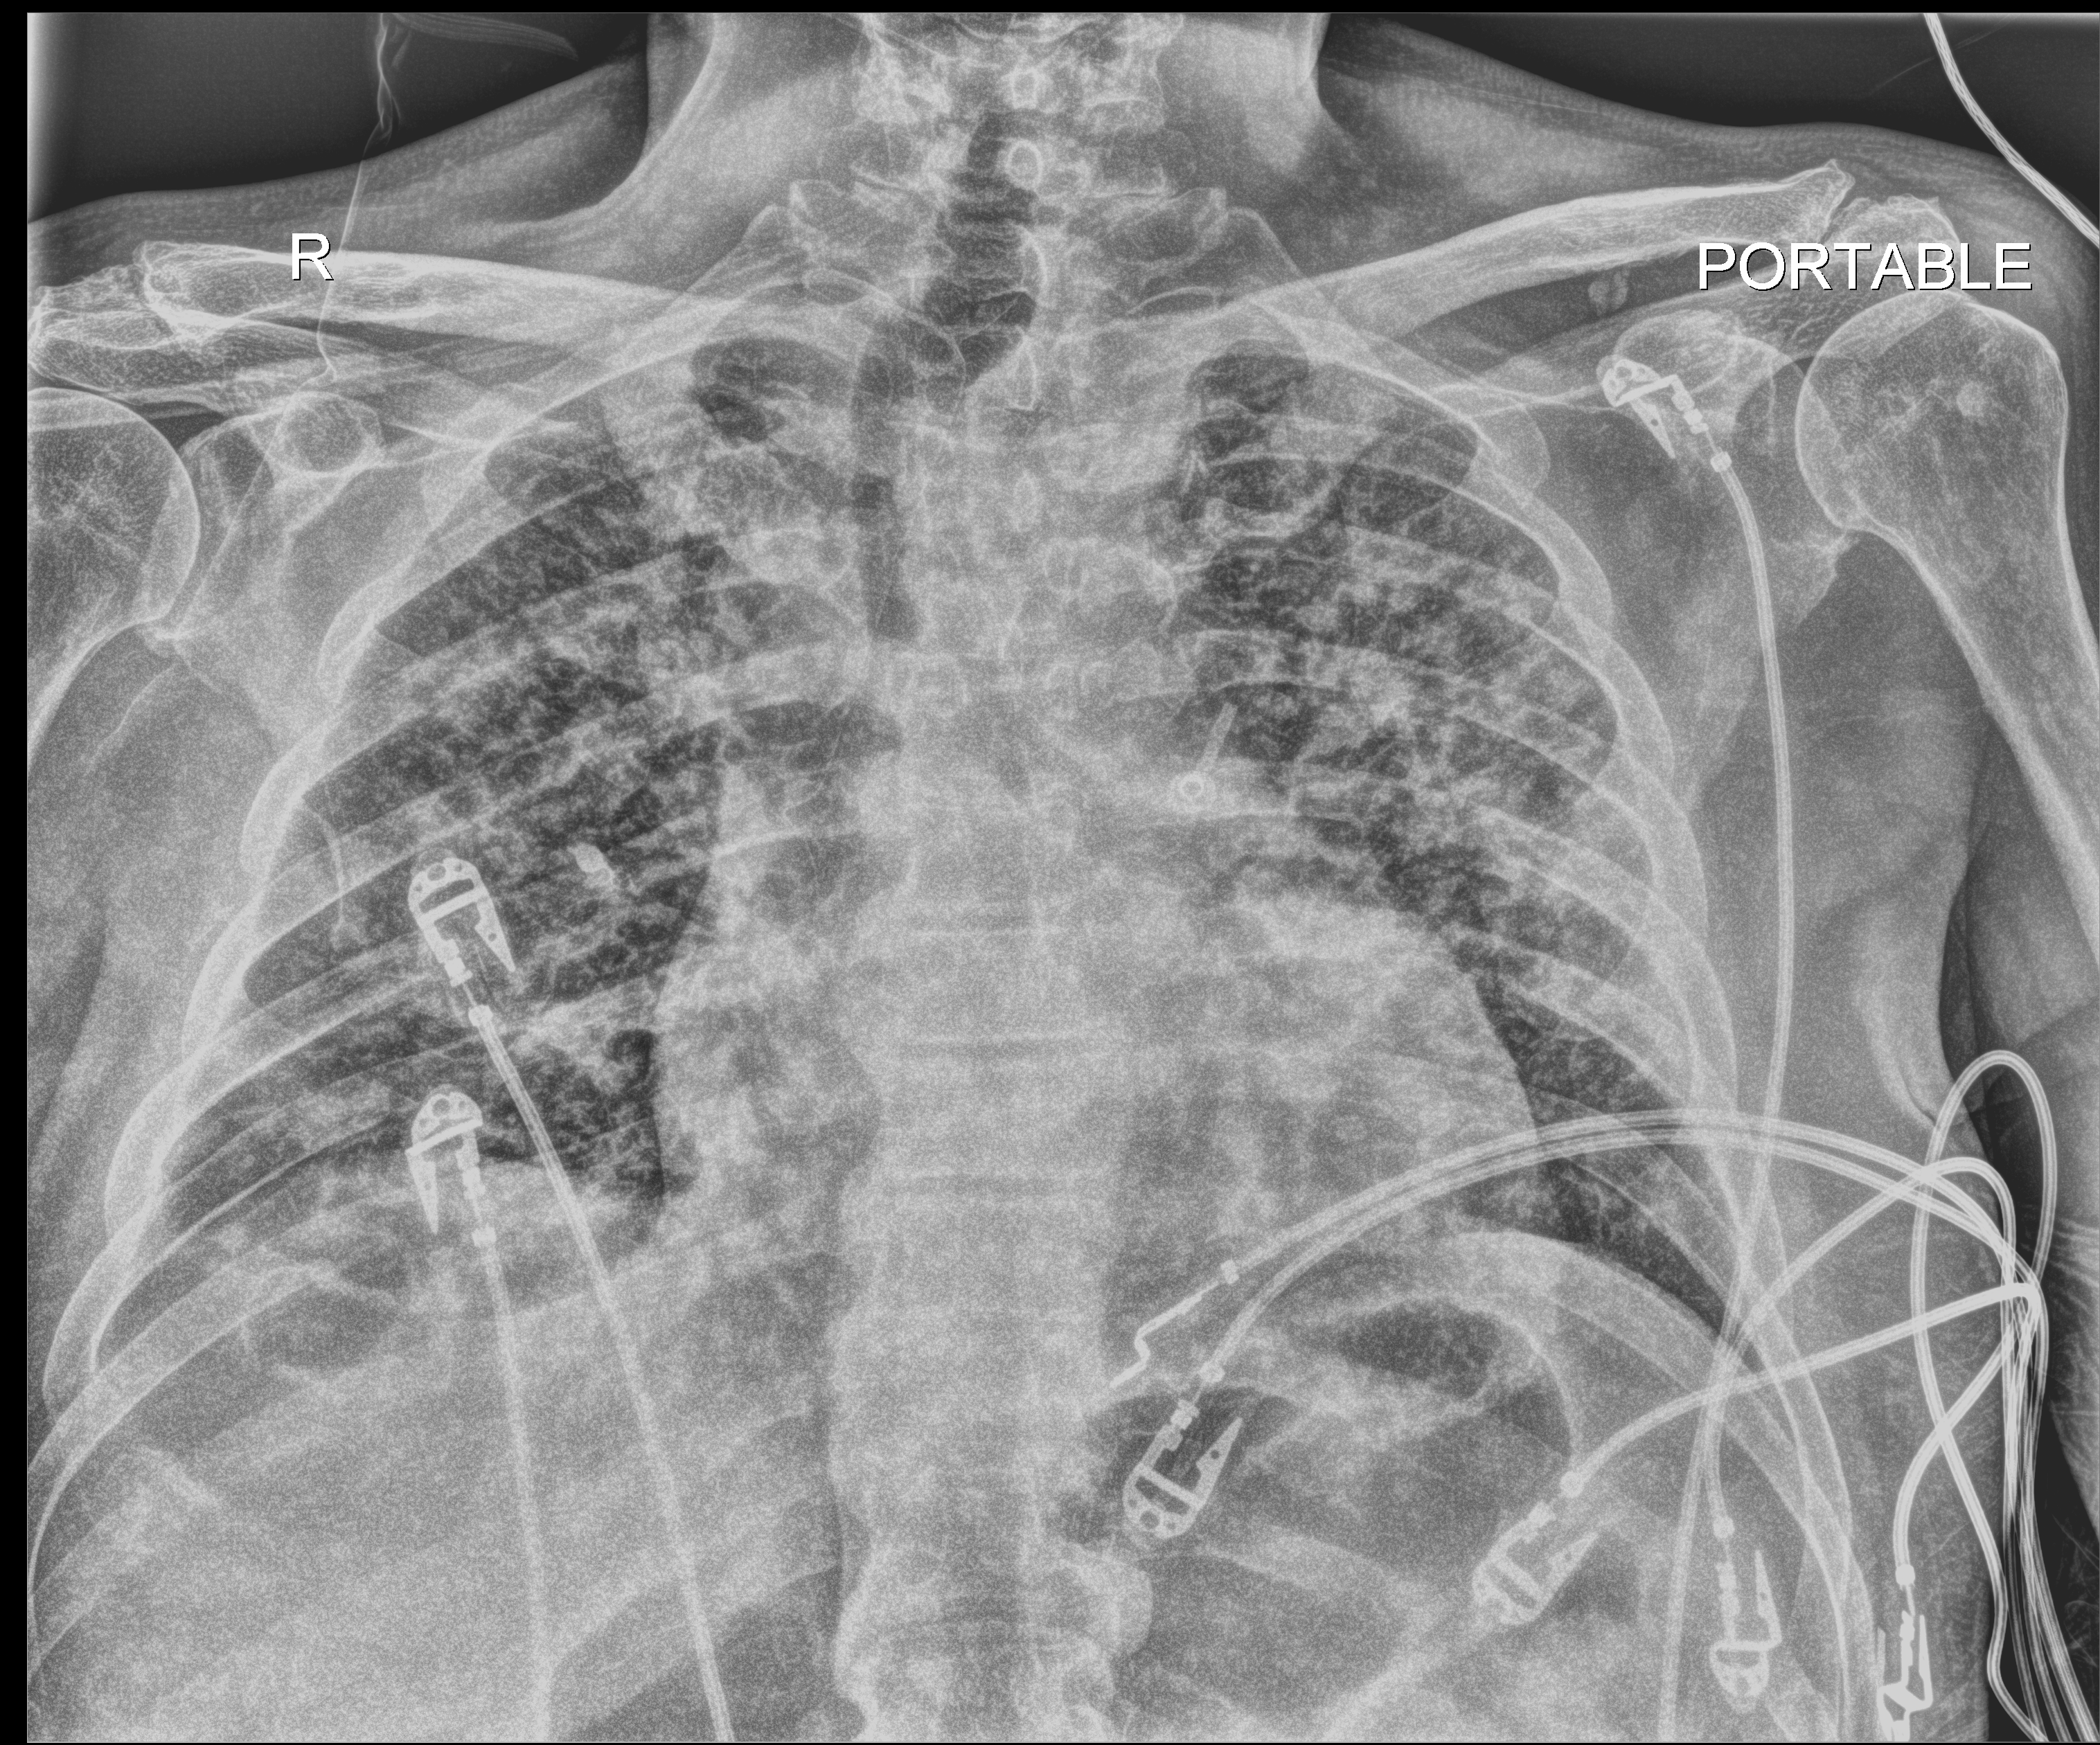
Chest radiograph (digital radiography), anteroposterior (AP) projection. Patient hospitalised with COVID-19; male, aged 18–59 years.
Admission-level facts for this patient (not findings on this image; timing relative to this image not recorded):
- smoking status (admission record): never